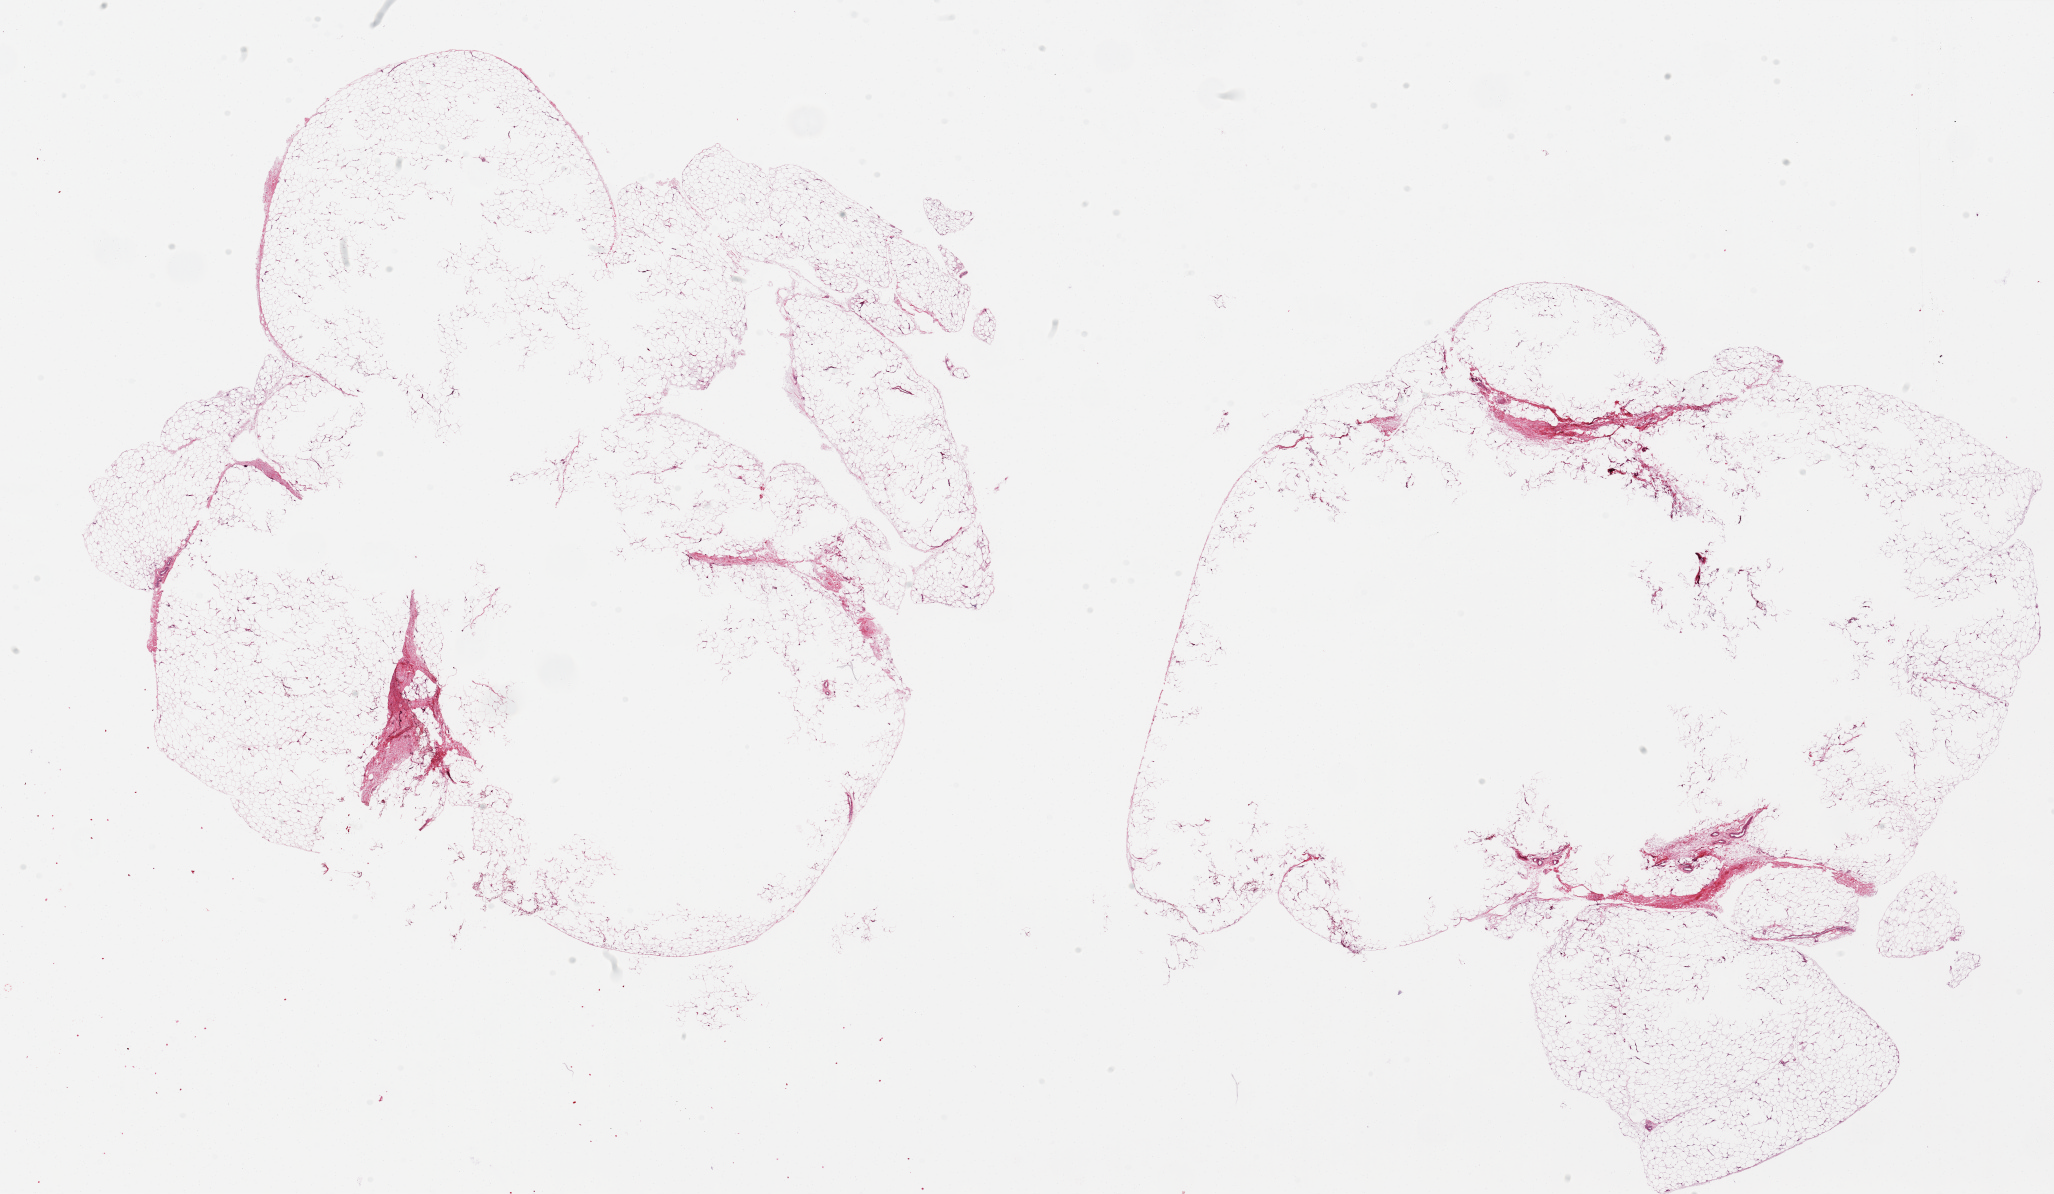
Haematoxylin and eosin whole-slide image, brightfield — whole scanned area (about 32.5 x 18.9 mm) shown as a low-resolution overview. PAXgene-fixed paraffin-embedded (PFPE) section. Sampled site (target tissue): adipose tissue. Tissue donor sample. Donor sex: female.
Pathologist's review note for this sample: 2 ~8x7mm aliquots, extreme separation falsely implies larger dimensions.